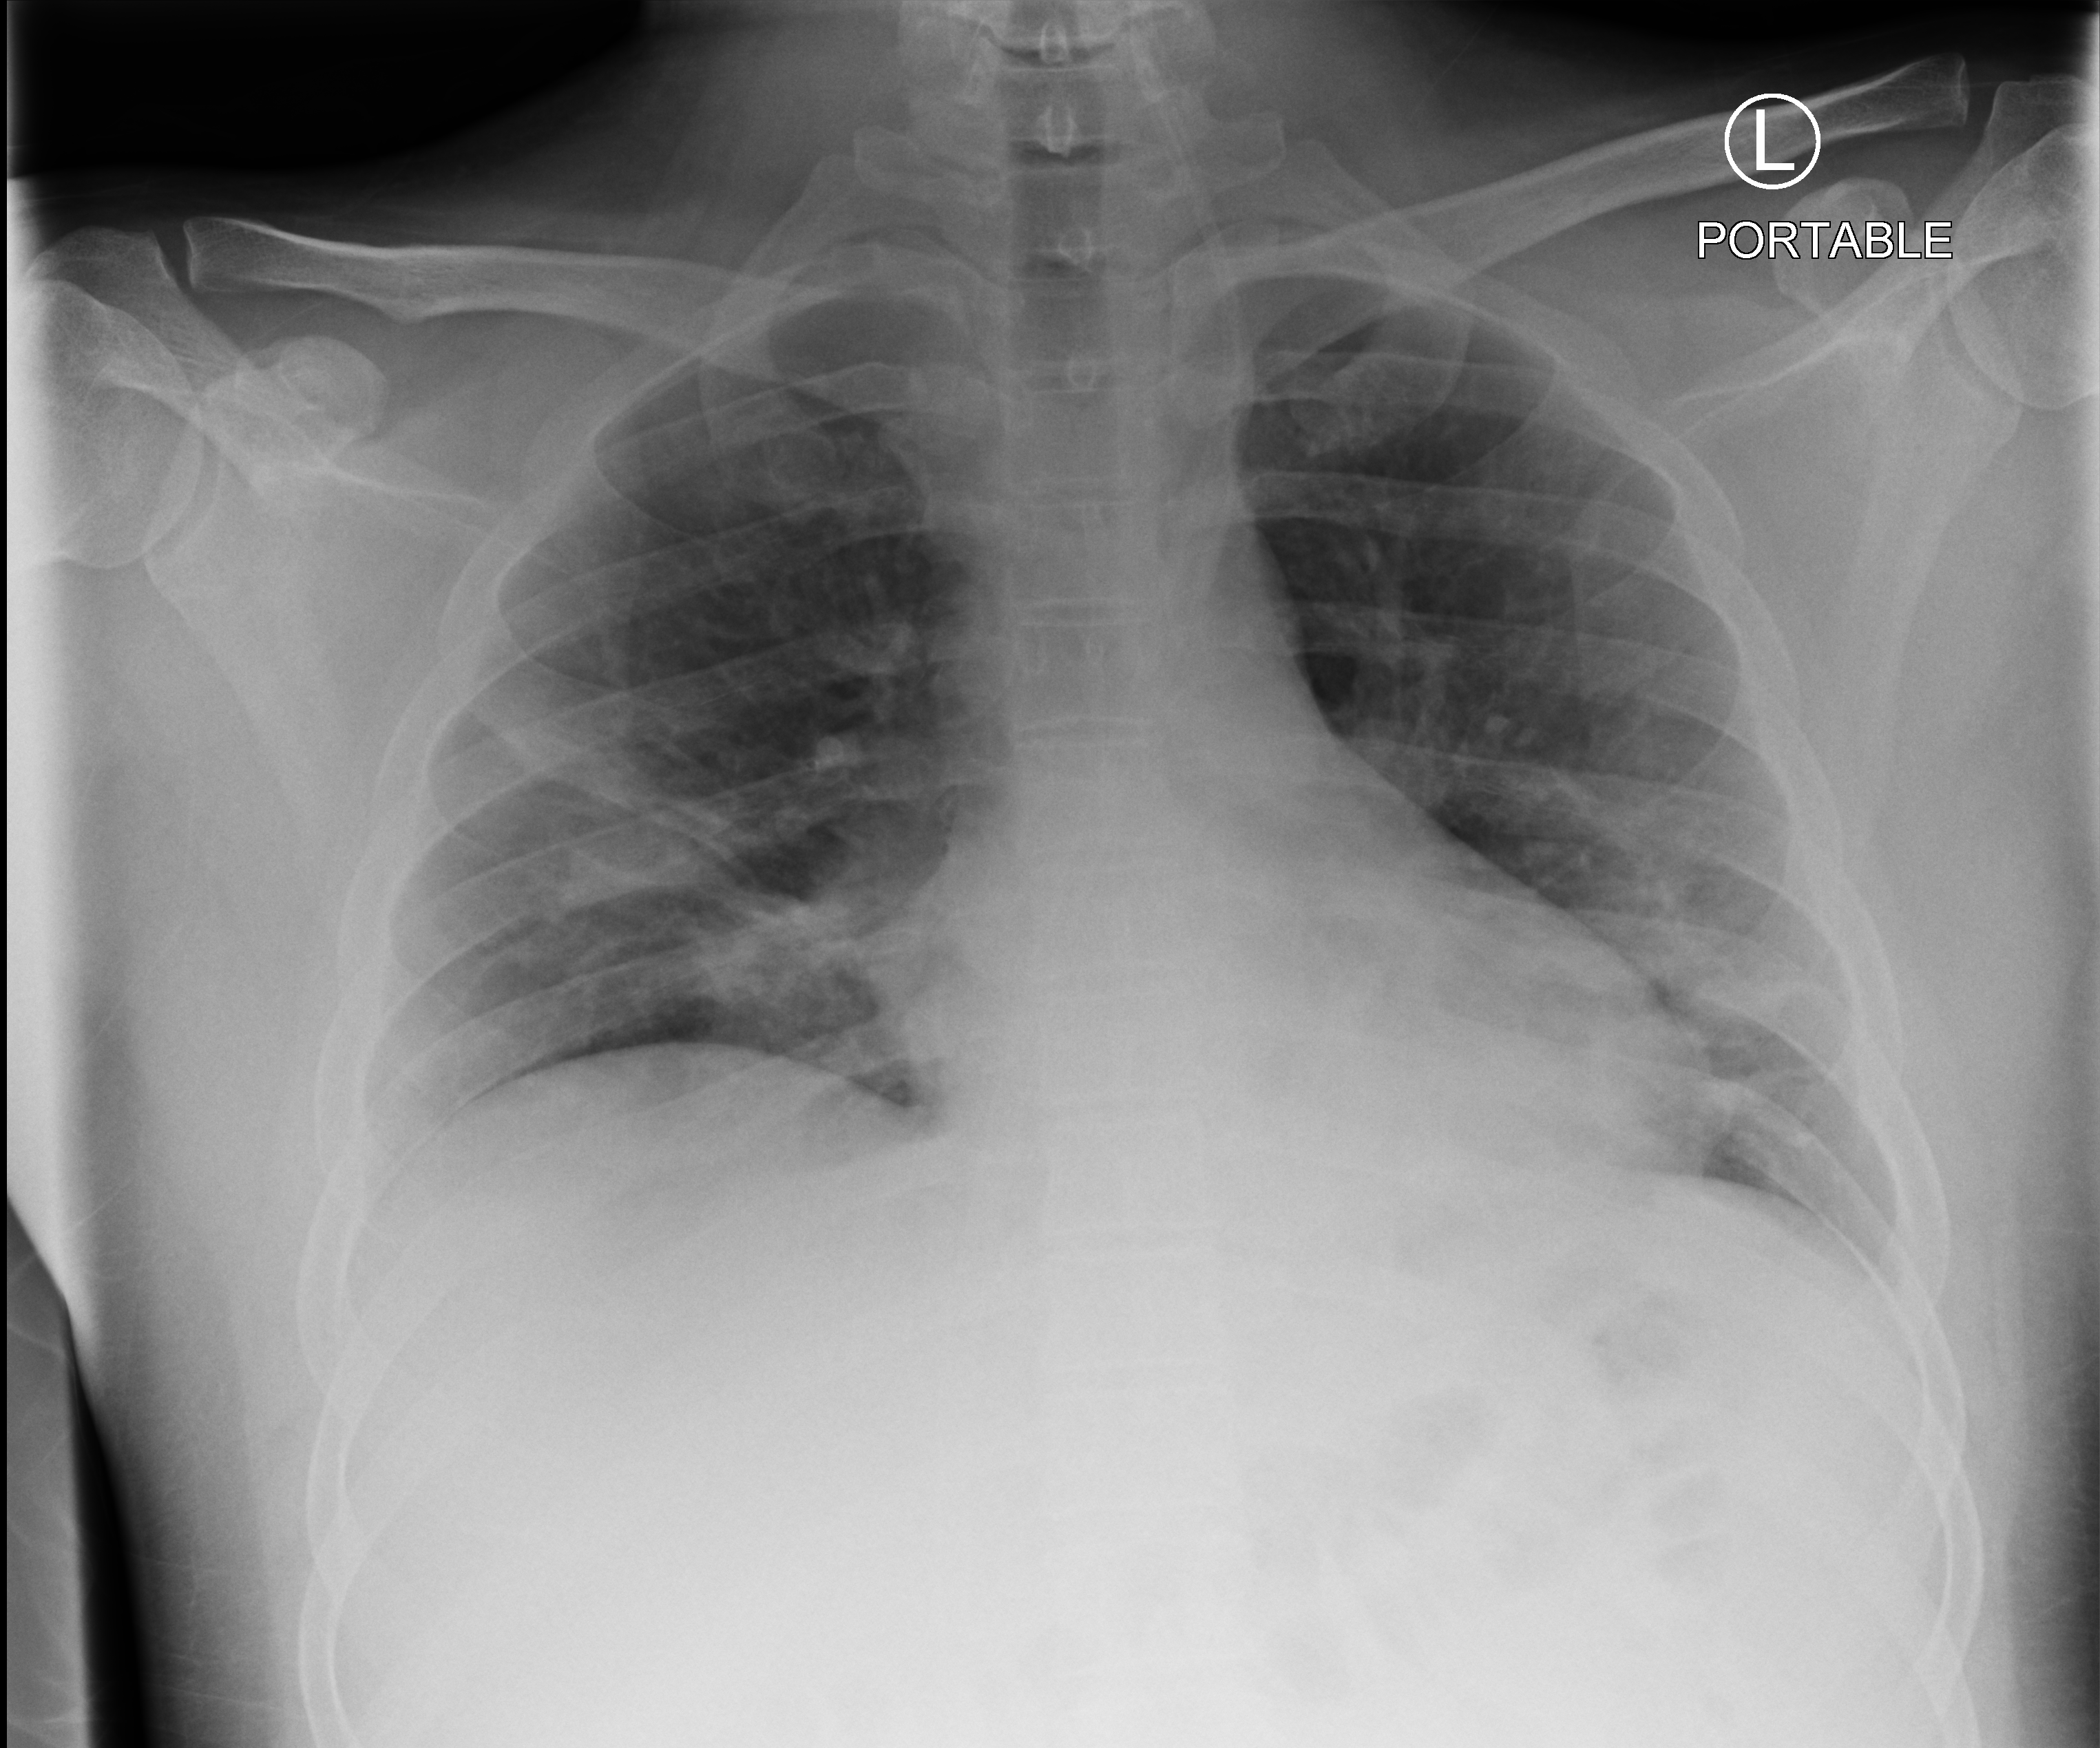
Bedside chest radiograph (computed radiography). Male patient hospitalised with COVID-19, age 18–59 years.
Hospital-stay facts (about this admission, not read from this image; timing relative to this image not recorded): admitted to intensive care during this hospital stay: yes; COPD (admission record): no.